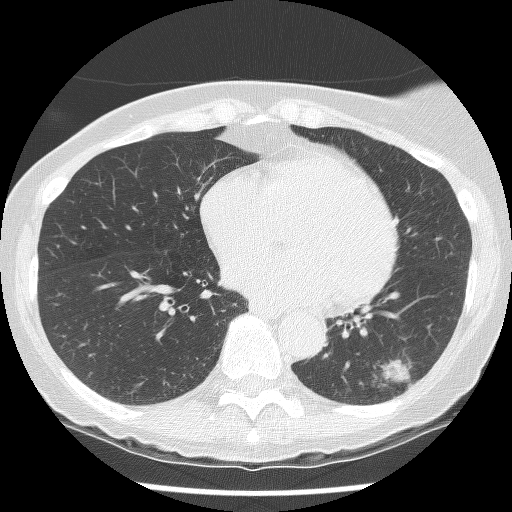
Axial slice from a low-dose chest CT screening exam. Second annual screen. Lung window (W 1500 / L -600 HU). 2.5 mm slice thickness. Slice 82 of 136 in the series. Female, age 61 years at enrolment. Current smoker at enrolment.
- Expert reader's lesion annotation, bounding box <335,336,434,419> (left, top, right, bottom; pixels).
- The screening reader recorded 2 non-calcified nodules or masses ≥4 mm on this exam; which of them this box marks is not recorded.
- Lung cancer was diagnosed 585 days after this screen (after the third annual screen): non-small cell carcinoma, left lower lobe, poorly differentiated (G3), stage IB (AJCC 6th edition), 100 mm at pathology.